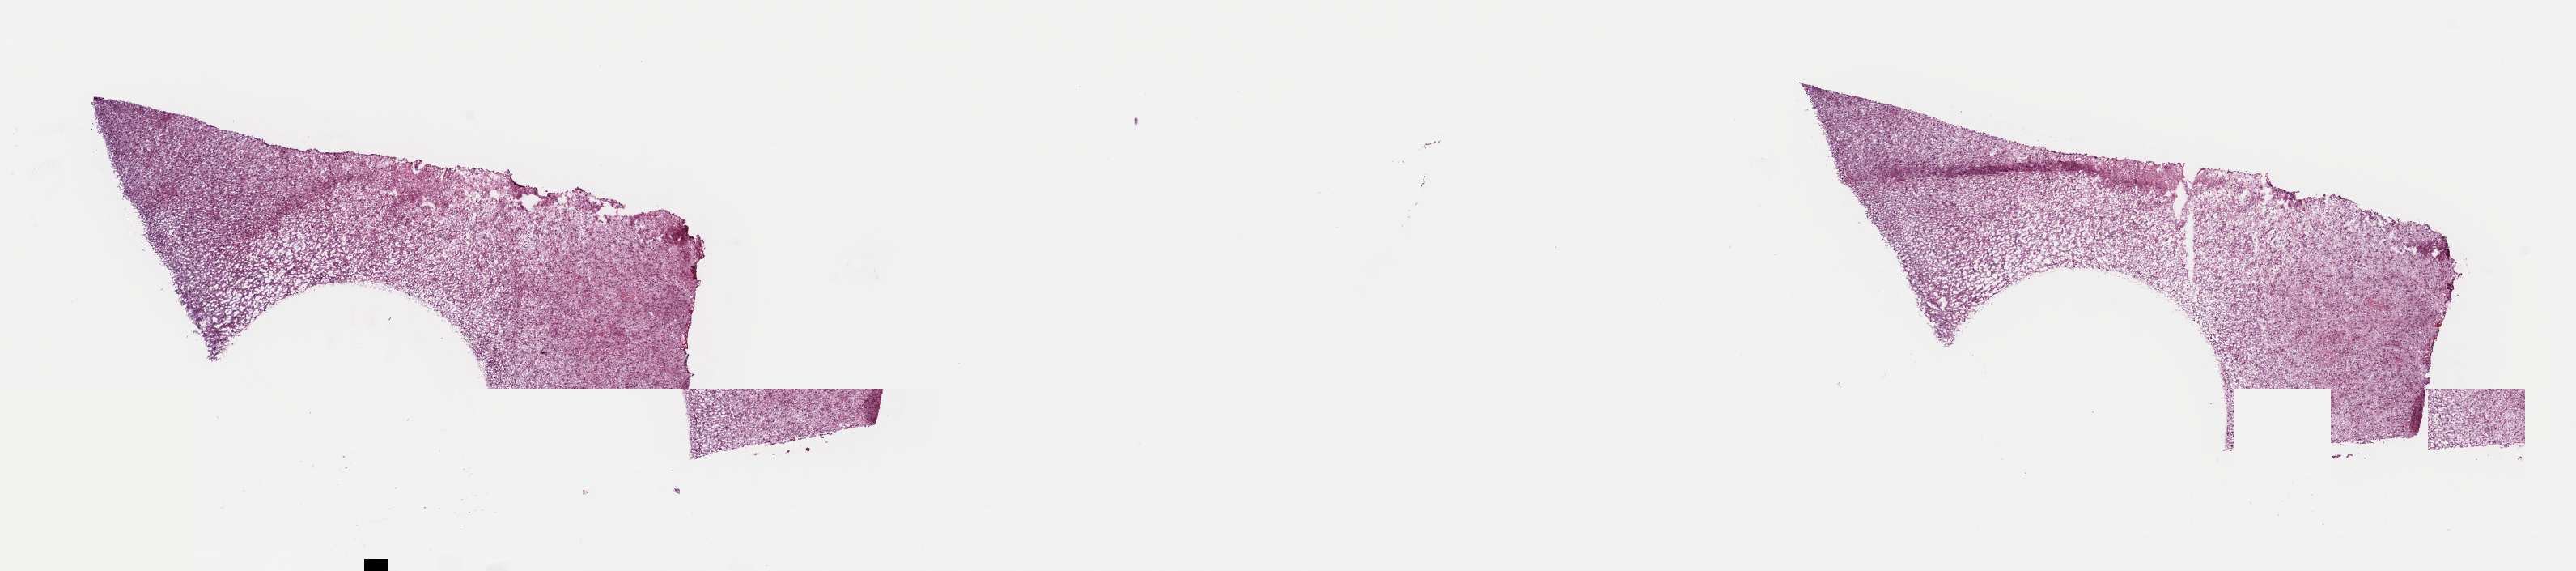
Hematoxylin and eosin (H&E) stained whole-slide image — whole scanned area (about 25.1 x 5.6 mm) shown as a low-resolution overview, frozen section from the top of the tissue portion, sample: primary tumour, brain. Male patient; age at initial diagnosis 29 years. Histologic grade: G3 (poorly differentiated). Pathologist review of this section (percent, as recorded): tumour cells 40%, tumour nuclei 80%, normal cells 10%, stromal cells 50%, necrosis 0%. Infiltration values recorded for this section: lymphocyte infiltration 0%, monocyte infiltration 0%, neutrophil infiltration 0%.
Histologic diagnosis: Astrocytoma, anaplastic (cerebrum). Laterality: left.